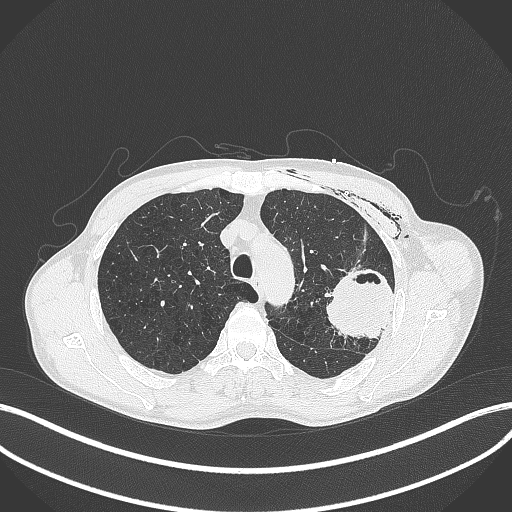
Chest CT, one axial slice. Slice 307 of 457 in the series (ordered by position). 120 kVp. Lung window (W 1500 / L -600 HU). 1 mm slice thickness. 512 × 512 image matrix, field of view 400 × 400 mm. Male patient, age 58 years. From the clinical record (not read from this slice): clinical TNM (as recorded): T3 N0 M0.
Outlined on this slice (bounding box drawn by a radiologist):
- lung tumour (recorded histology: adenocarcinoma): bounding box (x1, y1, x2, y2) in pixels: (323, 267, 401, 348)